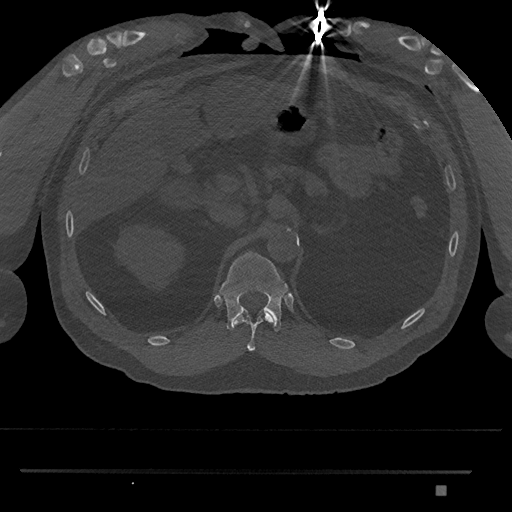
CT including the spine, one axial slice; position 908 of 1134 along the scan axis; 120 kVp; bone window (W 1800 / L 400 HU); 0.5 mm slice thickness; 512 × 512 image matrix. Patient: male, 65 years. Case-level facts recorded for this patient, not image findings: primary cancer: prostate.
Annotated regions visible in this slice (semi-automatically segmented with operator editing):
- T11 vertebra: bounding box [x1, y1, x2, y2] px = [235, 310, 273, 351]
- T12 vertebra: [219, 251, 288, 332]